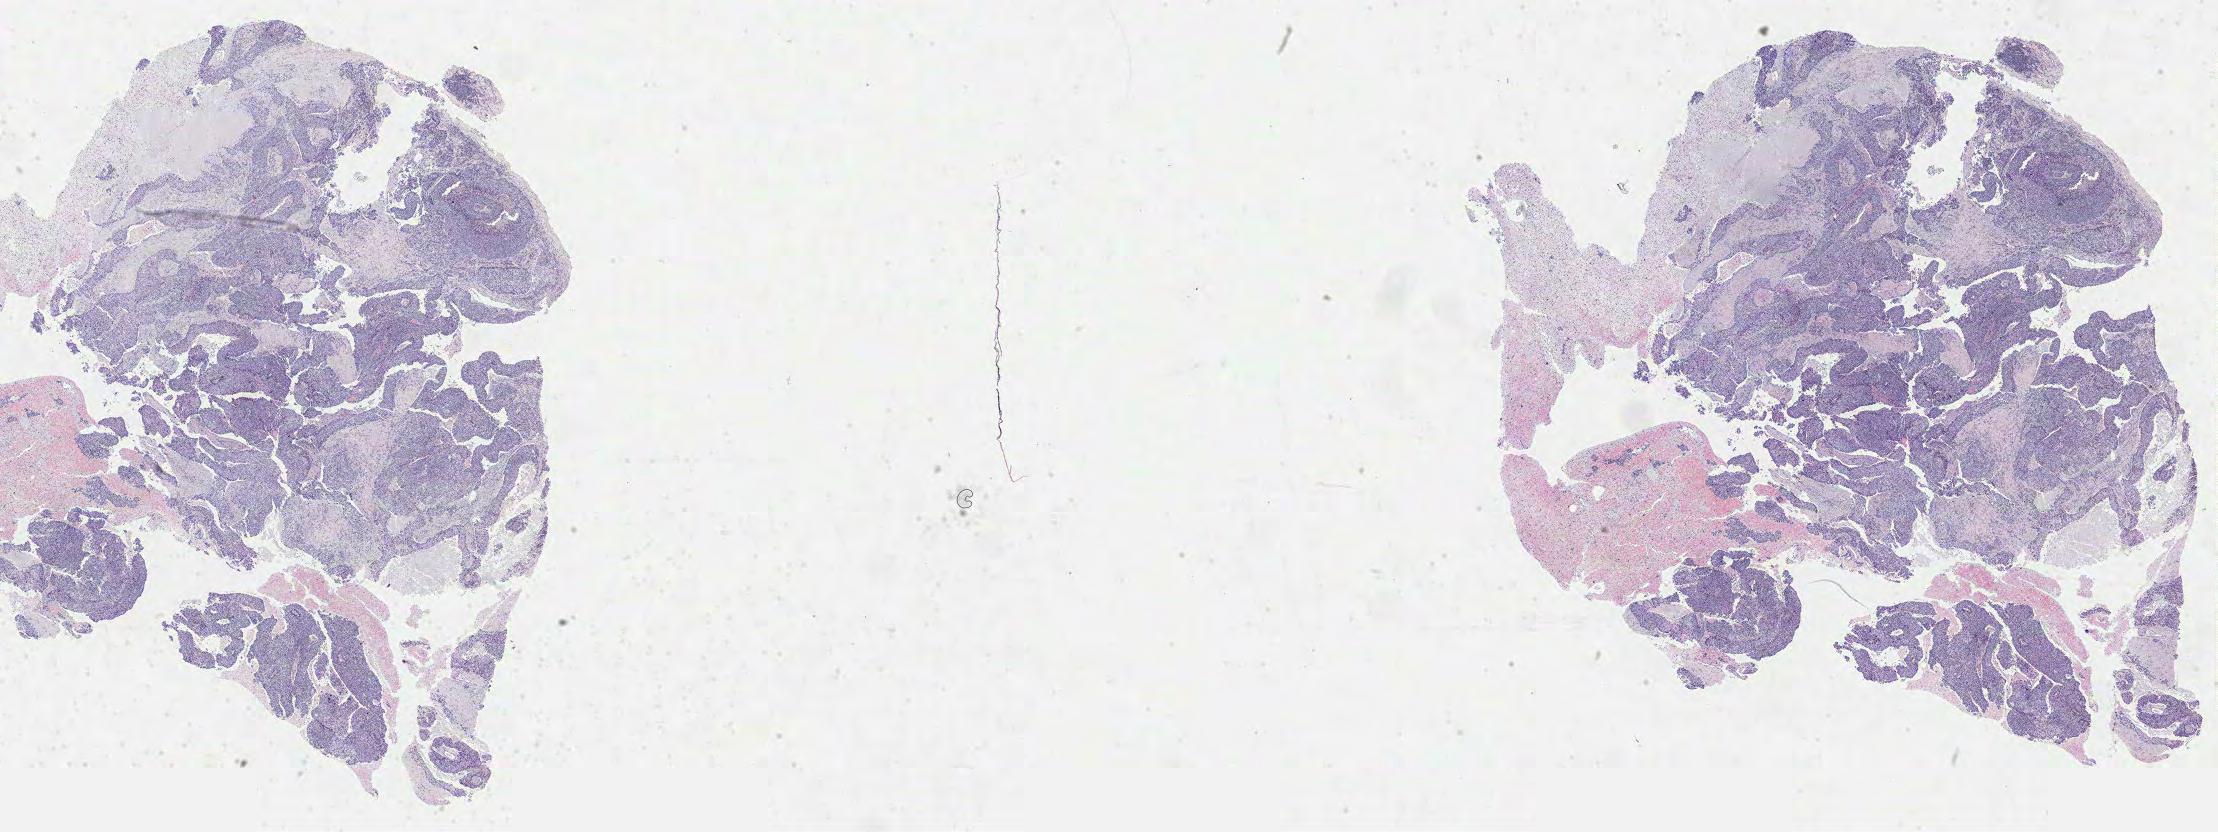
Whole-slide histology image, Hematoxylin and eosin (H&E) stained, shown as a low-resolution overview of the whole scanned area (about 35.8 x 13.4 mm, from a 40x scan), FFPE section, primary tumour sample from the lung. Male patient; age at initial diagnosis 68 years.
• diagnosis: Squamous cell carcinoma, NOS
• AJCC pathologic stage: IIIB (6th edition)
• laterality: right